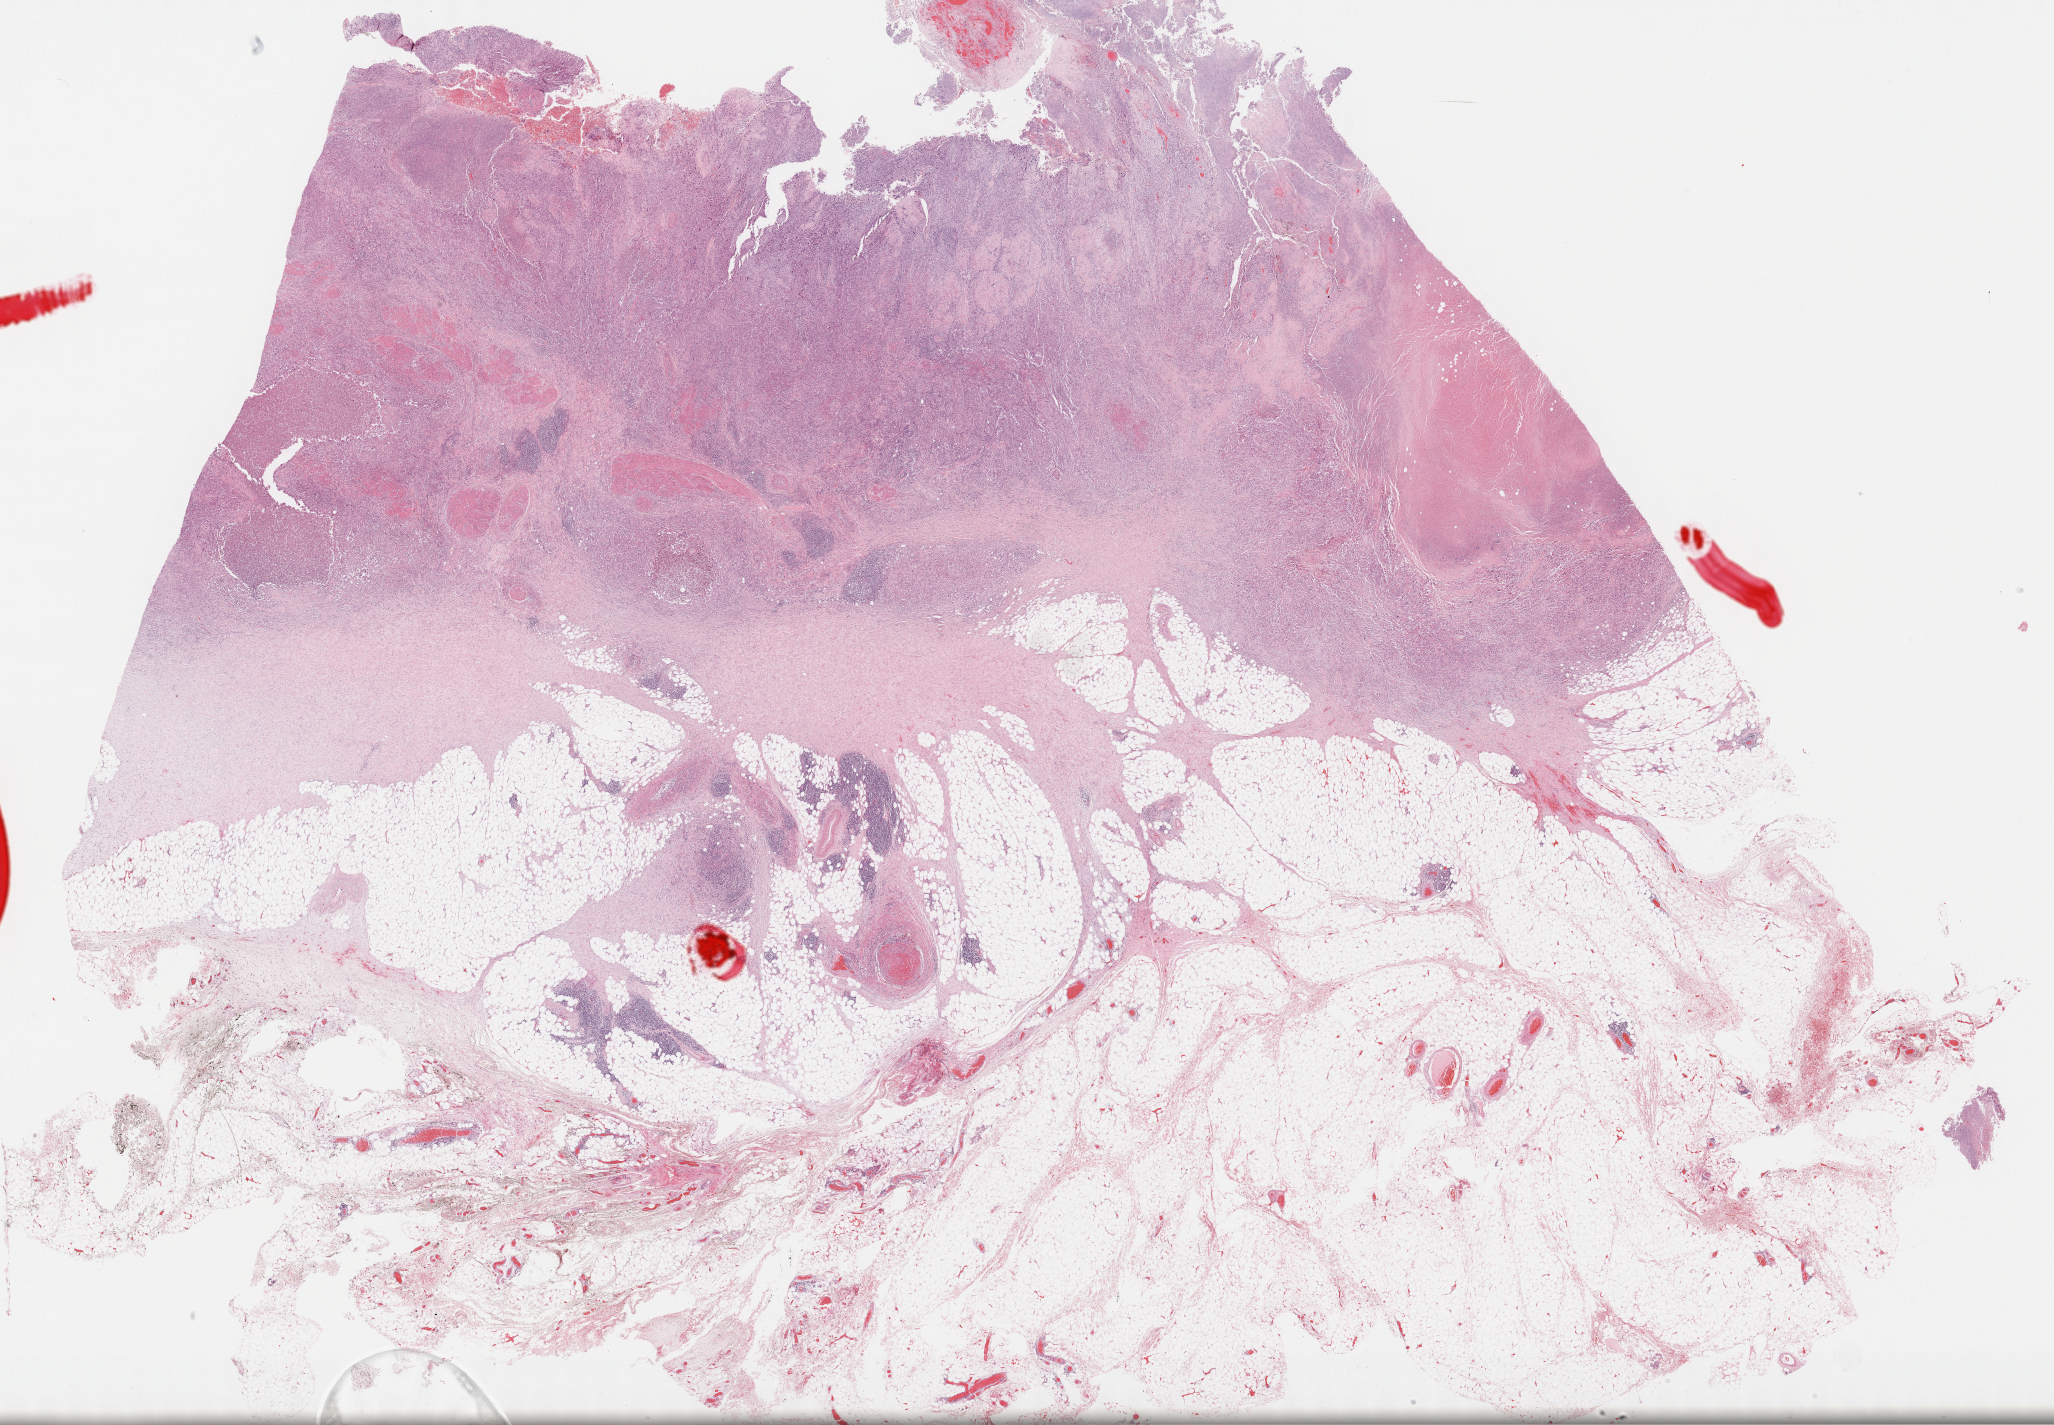
Whole-slide histology image, Hematoxylin and eosin (H&E) stained, whole scanned area (about 33.2 x 23.0 mm) shown as a low-resolution overview; formalin-fixed paraffin-embedded (FFPE) diagnostic section; primary tumour sample from the bladder. Patient: female, age at initial diagnosis 61 years.
Pathologic diagnosis: Transitional cell carcinoma.